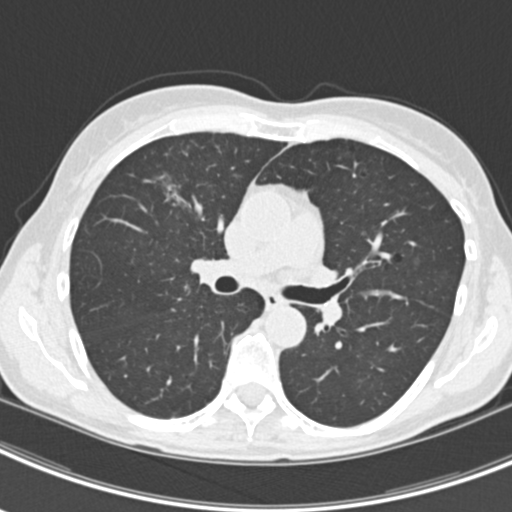
Axial slice from a low-dose chest CT screening exam; second annual screen; lung window (W 1500 / L -600 HU); 2 mm slice thickness; standard (soft-tissue) reconstruction kernel (B30f); slice 80 of 219 in the series. Female participant, aged 63 years at enrolment.
Expert-annotated lung lesion, bounding box (x1, y1, x2, y2) in pixels: (153, 169, 212, 224). The screening reader recorded 9 non-calcified nodules or masses ≥4 mm on this exam; which of them this box marks is not recorded. Official screen result: positive, other. Lung cancer was diagnosed 408 days after this screen (after the third annual screen): bronchiolo-alveolar adenocarcinoma, NOS, right upper lobe, right middle lobe, right lower lobe, left upper lobe, left lower lobe, moderately differentiated (G2), stage IV (AJCC 6th edition).